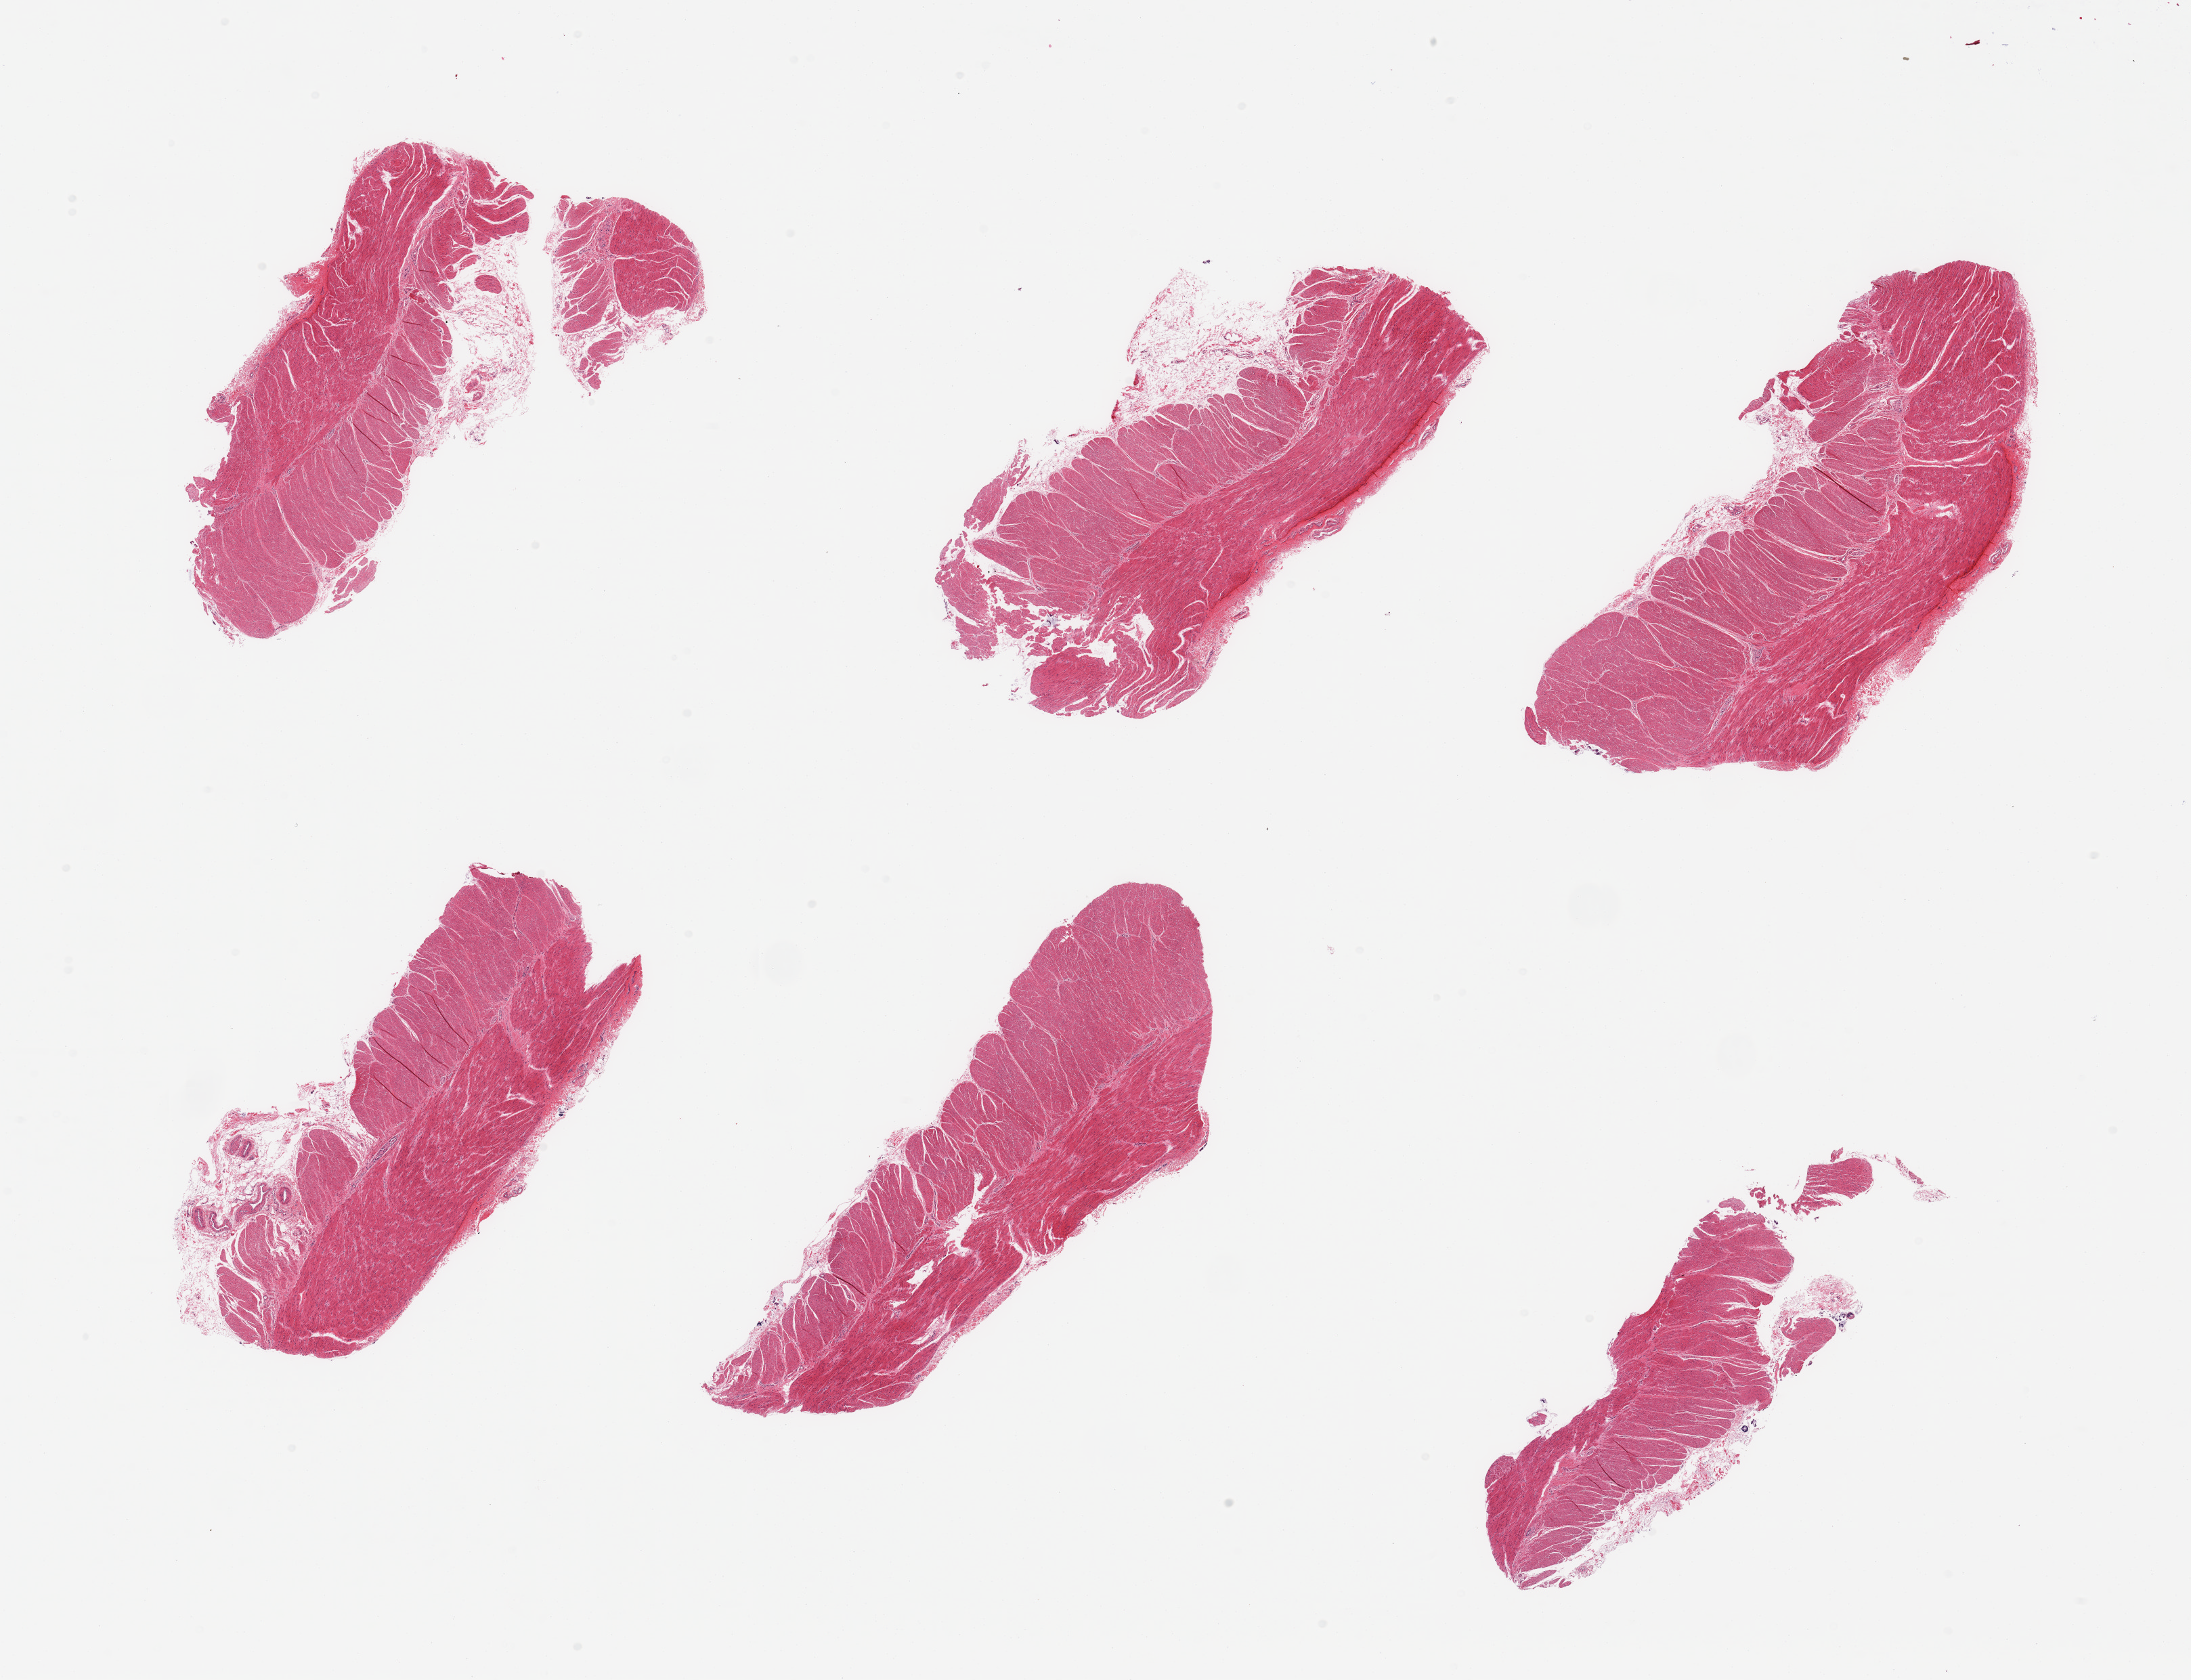
Digitized hematoxylin and eosin (H&E)-stained section, brightfield, a low-resolution overview of the entire scanned area, about 25.6 x 19.6 mm; PAXgene-fixed, paraffin-embedded tissue; sampled site (target tissue): sigmoid colon; tissue donor sample. Donor: female.
Review note (as recorded): 6 pieces; target muscularis with small attachment of fat/vessels.